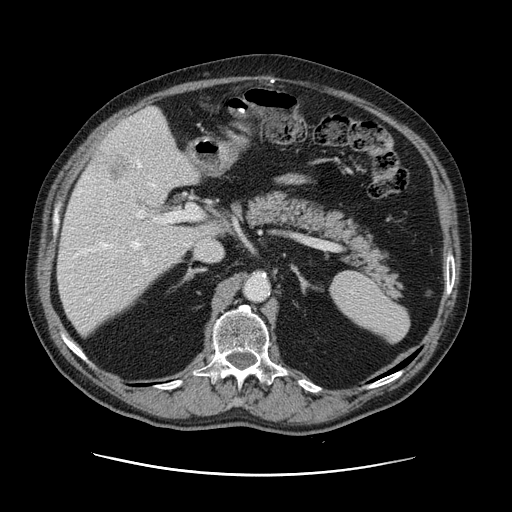
Contrast-enhanced abdominal CT, one axial slice. Position 74 of 141 along the scan axis. 120 kVp. Intravenous contrast given. Soft-tissue window (W 400 / L 40 HU). 2.5 mm slice thickness. 512 × 512 image matrix, field of view 395 × 395 mm. Male patient, age 72 years. From the clinical record (not read from this slice): diagnosis: colorectal cancer liver metastases, imaged before liver resection; multiple liver metastases: yes; largest metastasis: 5.4 cm; disease in both lobes: yes.
Outlined on this slice (expert manual segmentation):
- hepatic veins: bounding box (x1, y1, x2, y2) in pixels: (100, 161, 155, 250)
- liver: (58, 108, 219, 334)
- planned liver remnant (the part of the liver to remain after resection): (58, 172, 220, 334)
- portal vein (with intrahepatic branches): (88, 200, 202, 301)
- liver metastasis: (107, 163, 126, 185)